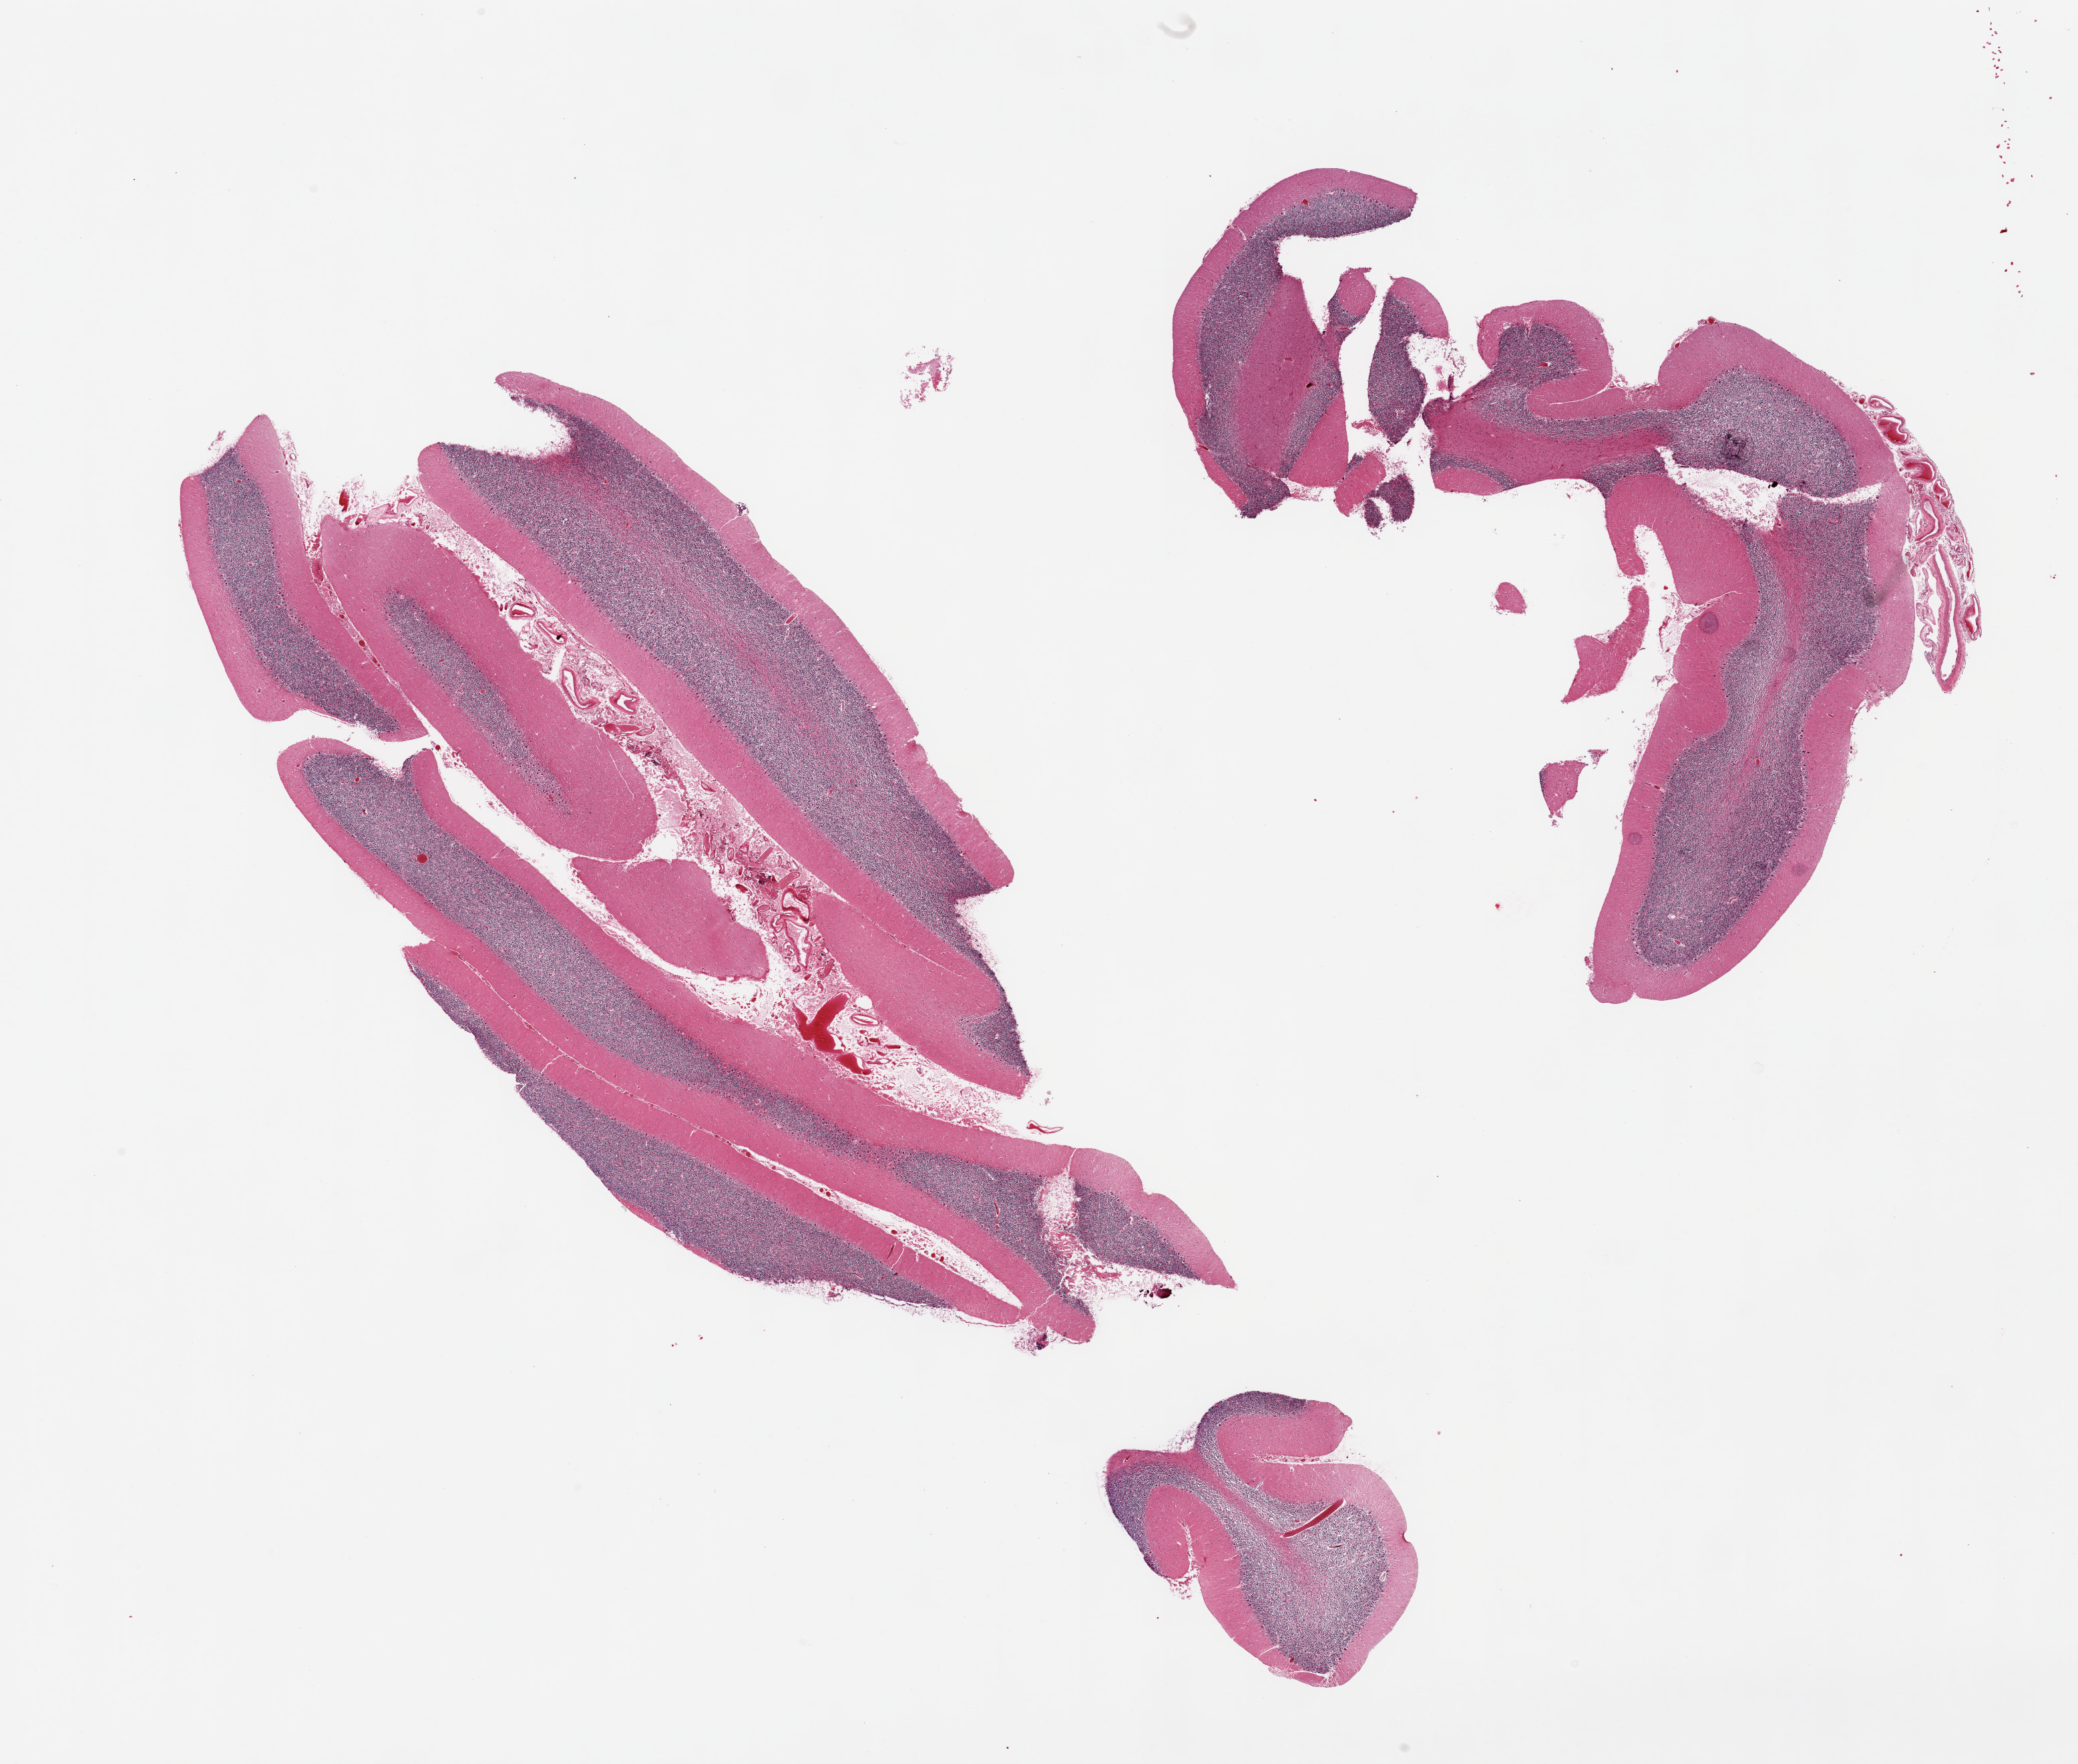
Whole-slide image, H&E stain, brightfield, a low-resolution overview of the entire scanned area, about 24.6 x 20.9 mm (acquisition: 20x scan). PAXgene-fixed paraffin-embedded (PFPE) section. Sampled site (target tissue): cerebellum. Donor tissue sample. Donor: male.
Reviewer comment on this tissue sample: 2 fragmented pieces with focal adherent meninges.